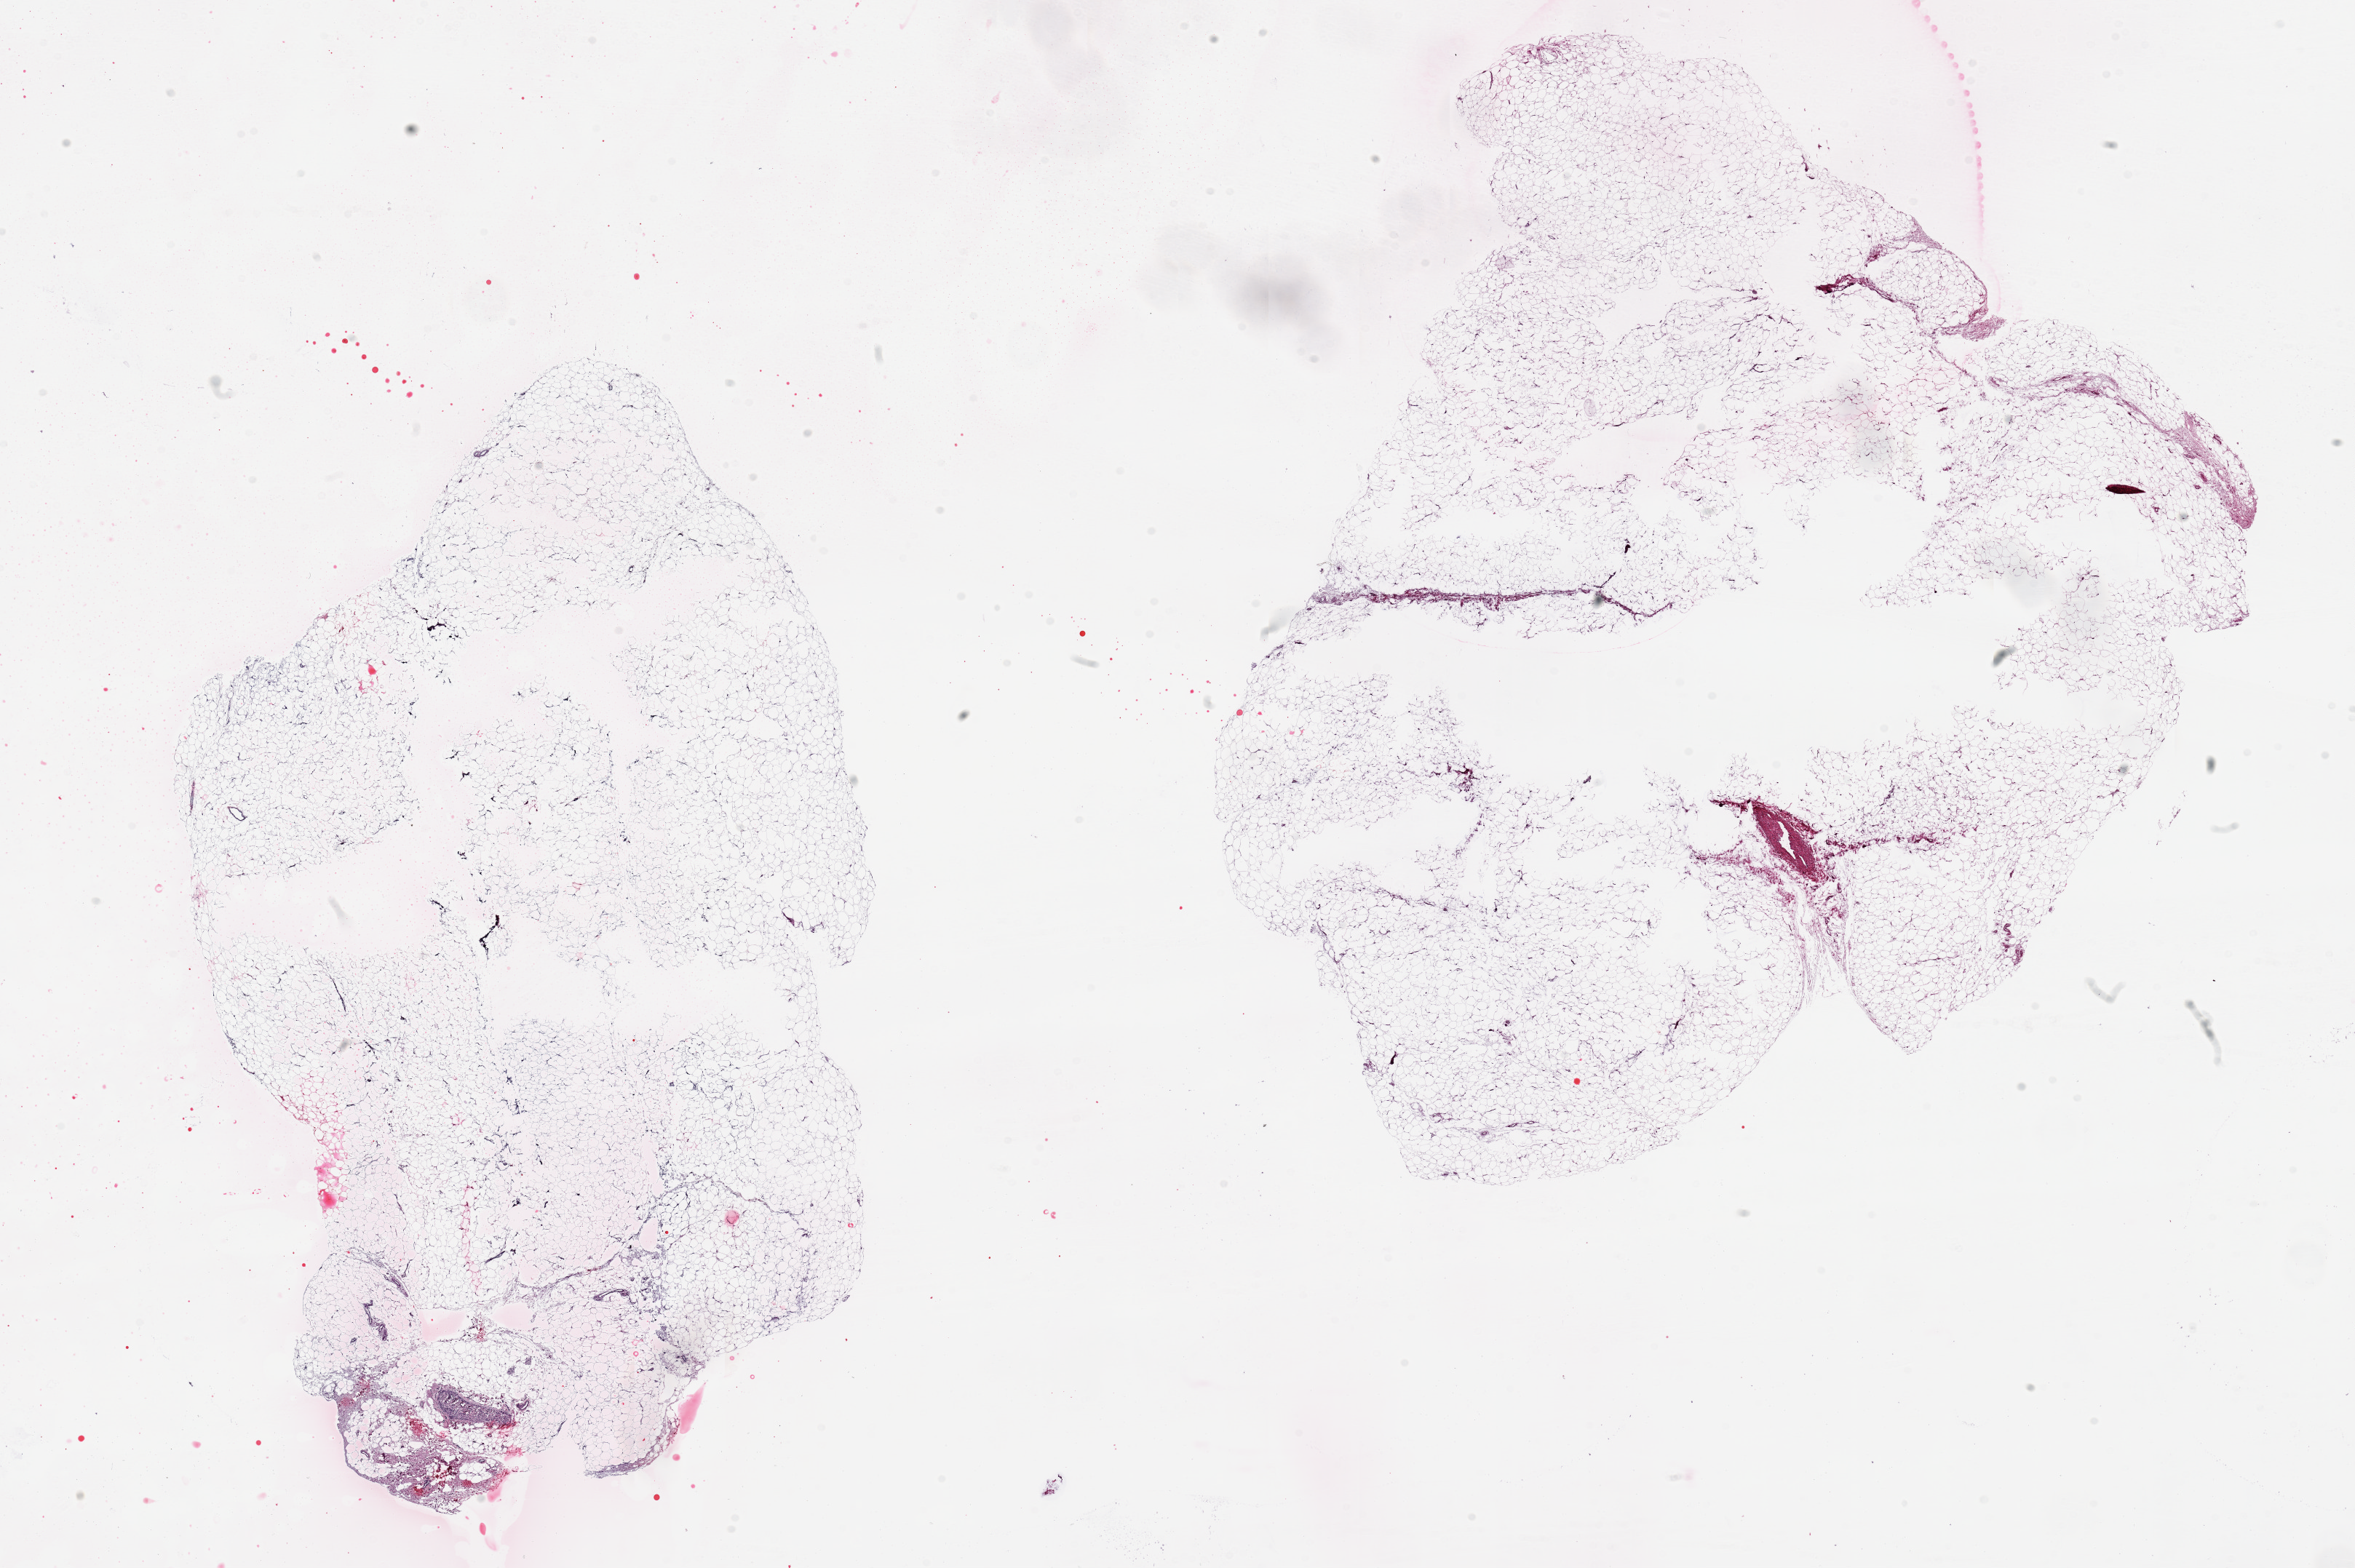
Digitized haematoxylin and eosin-stained section, low-resolution overview of the scanned area, about 25.6 x 17.0 mm, PAXgene-fixed, paraffin-embedded tissue, section of adipose tissue (target tissue), donor tissue sample.
* review note (as recorded): 2 overly large pieces, 12x11 and 12.6x7 mm. Both with focal central under-fixation. Staining debris